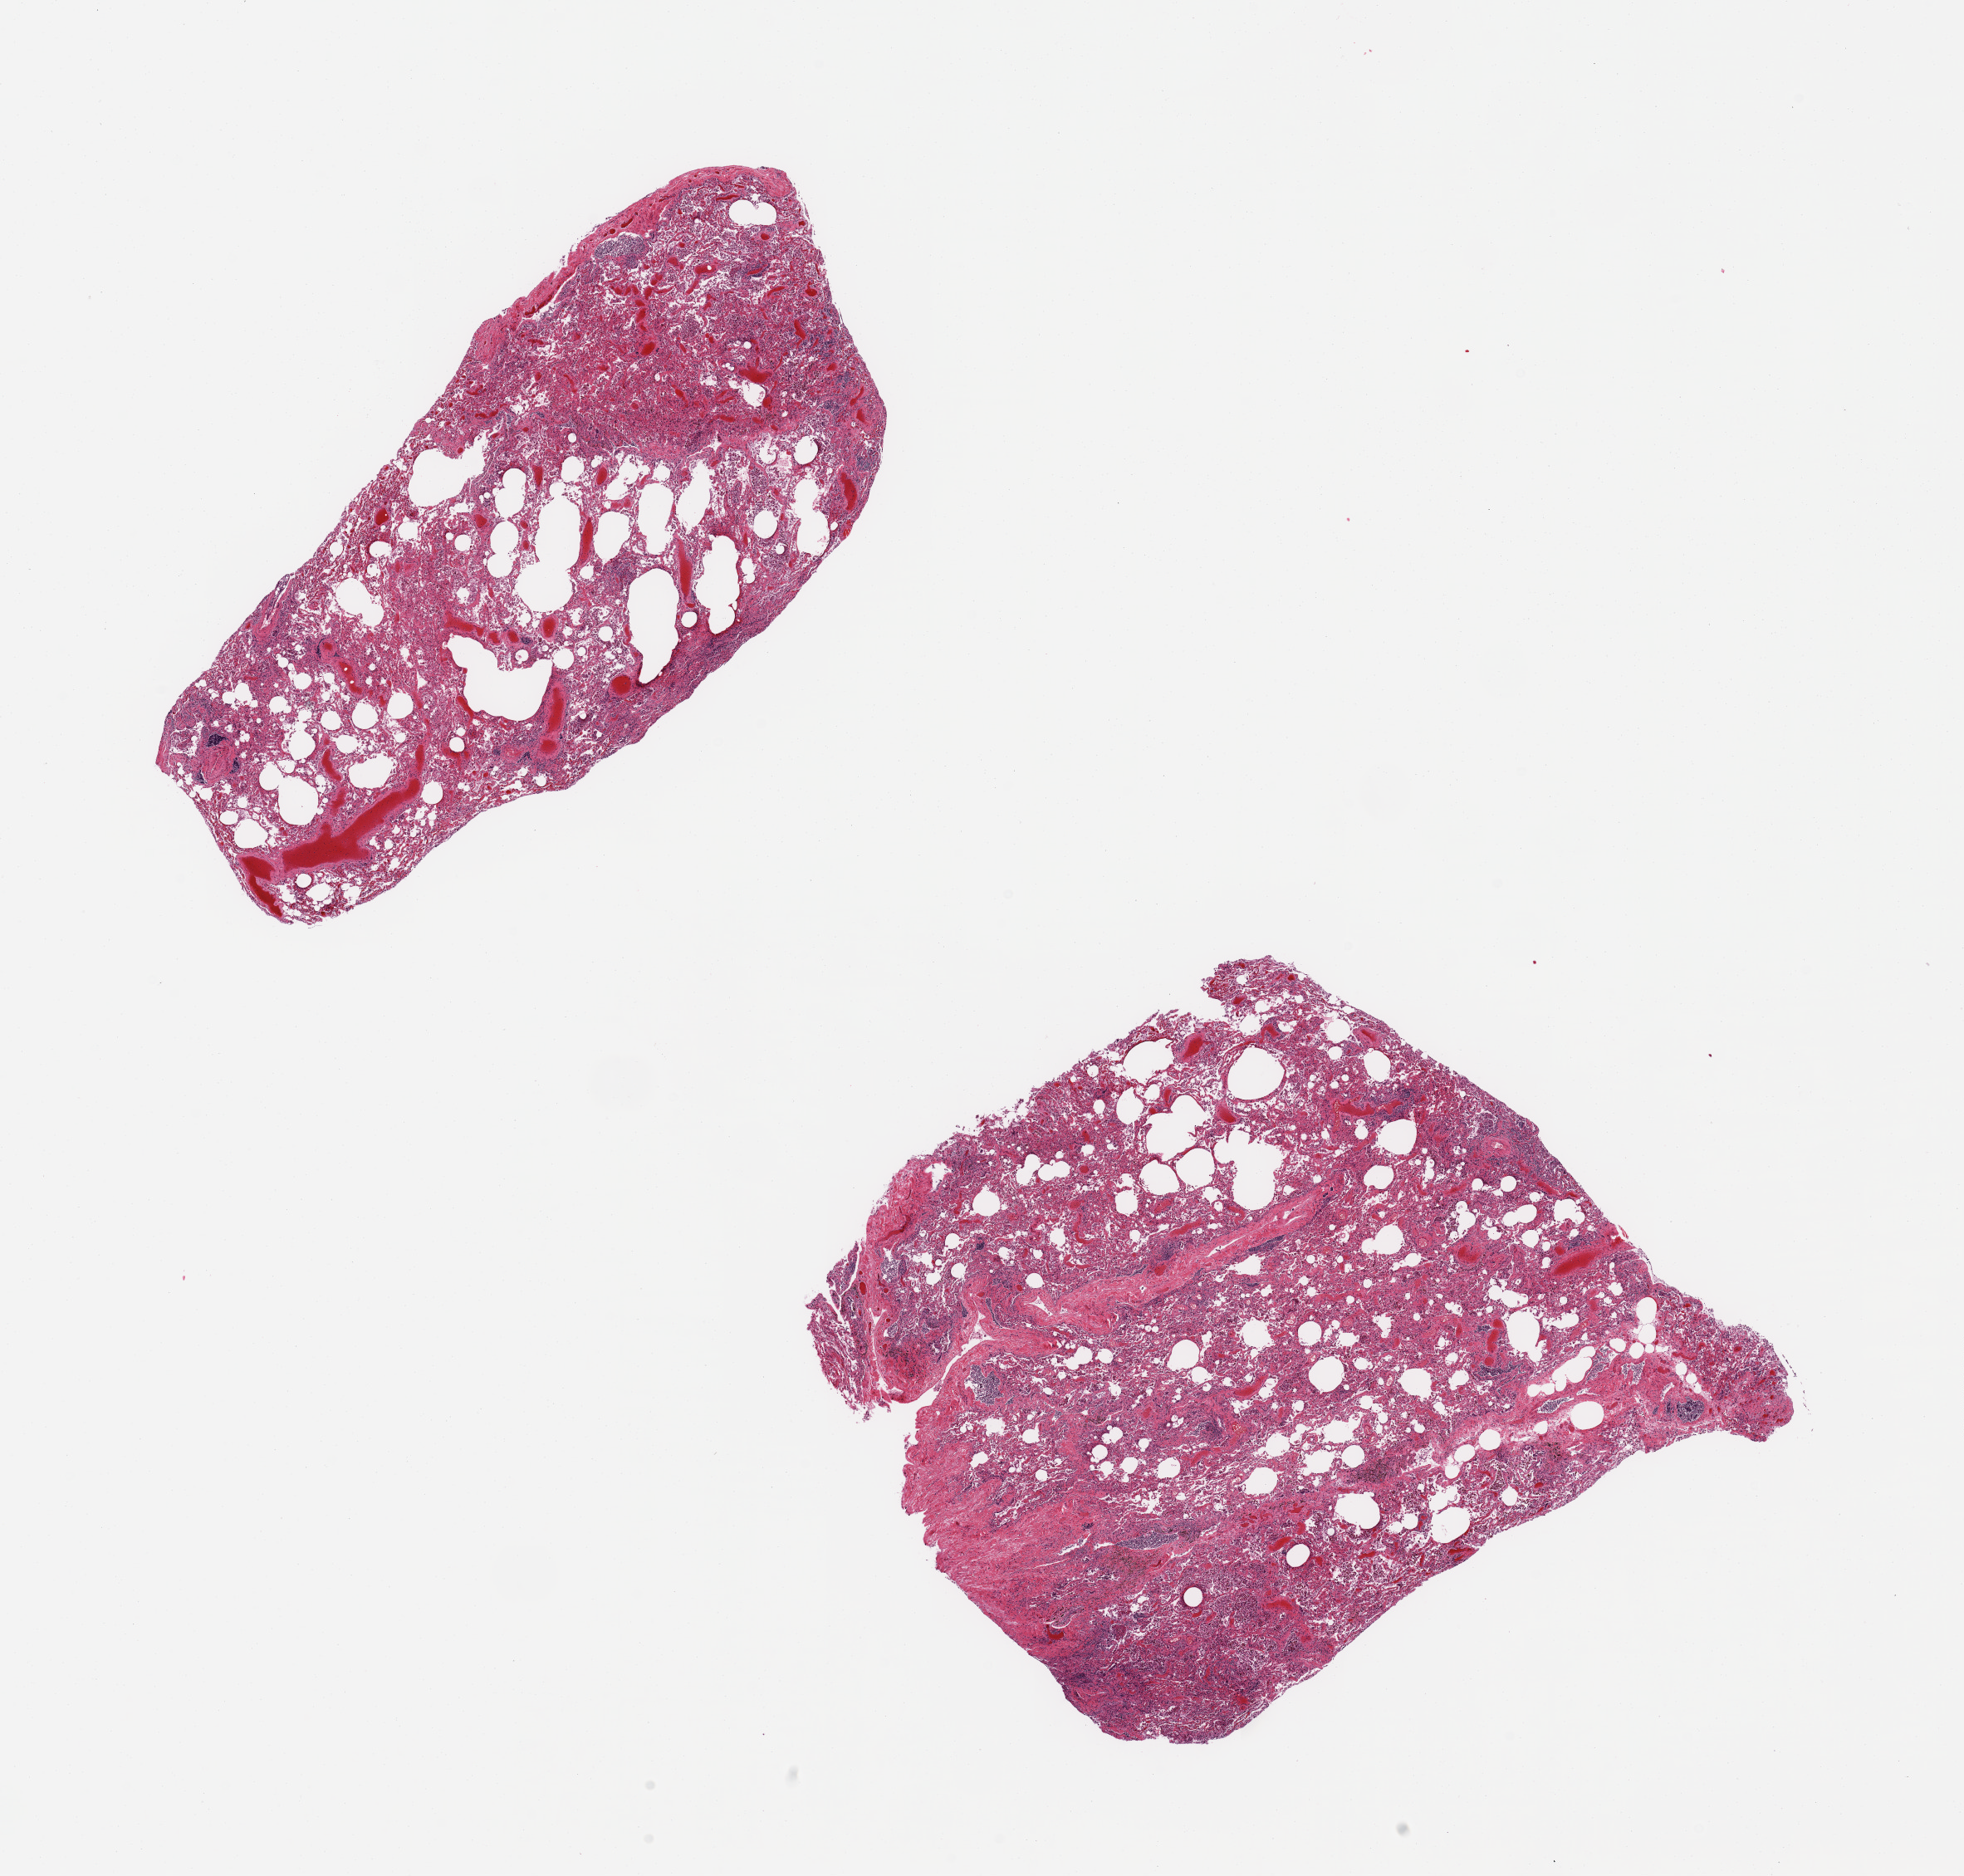
Whole-slide image, haematoxylin and eosin stain, brightfield, shown as a low-resolution overview of the whole scanned area (about 18.7 x 17.9 mm); PAXgene-fixed, paraffin-embedded tissue; target tissue: lung; donor tissue sample. Donor: male.
• review note (as recorded): 2 pieces; area of subpleural fibrosis at edge of 1 piece (10% of area); numerous alveolar macrophages